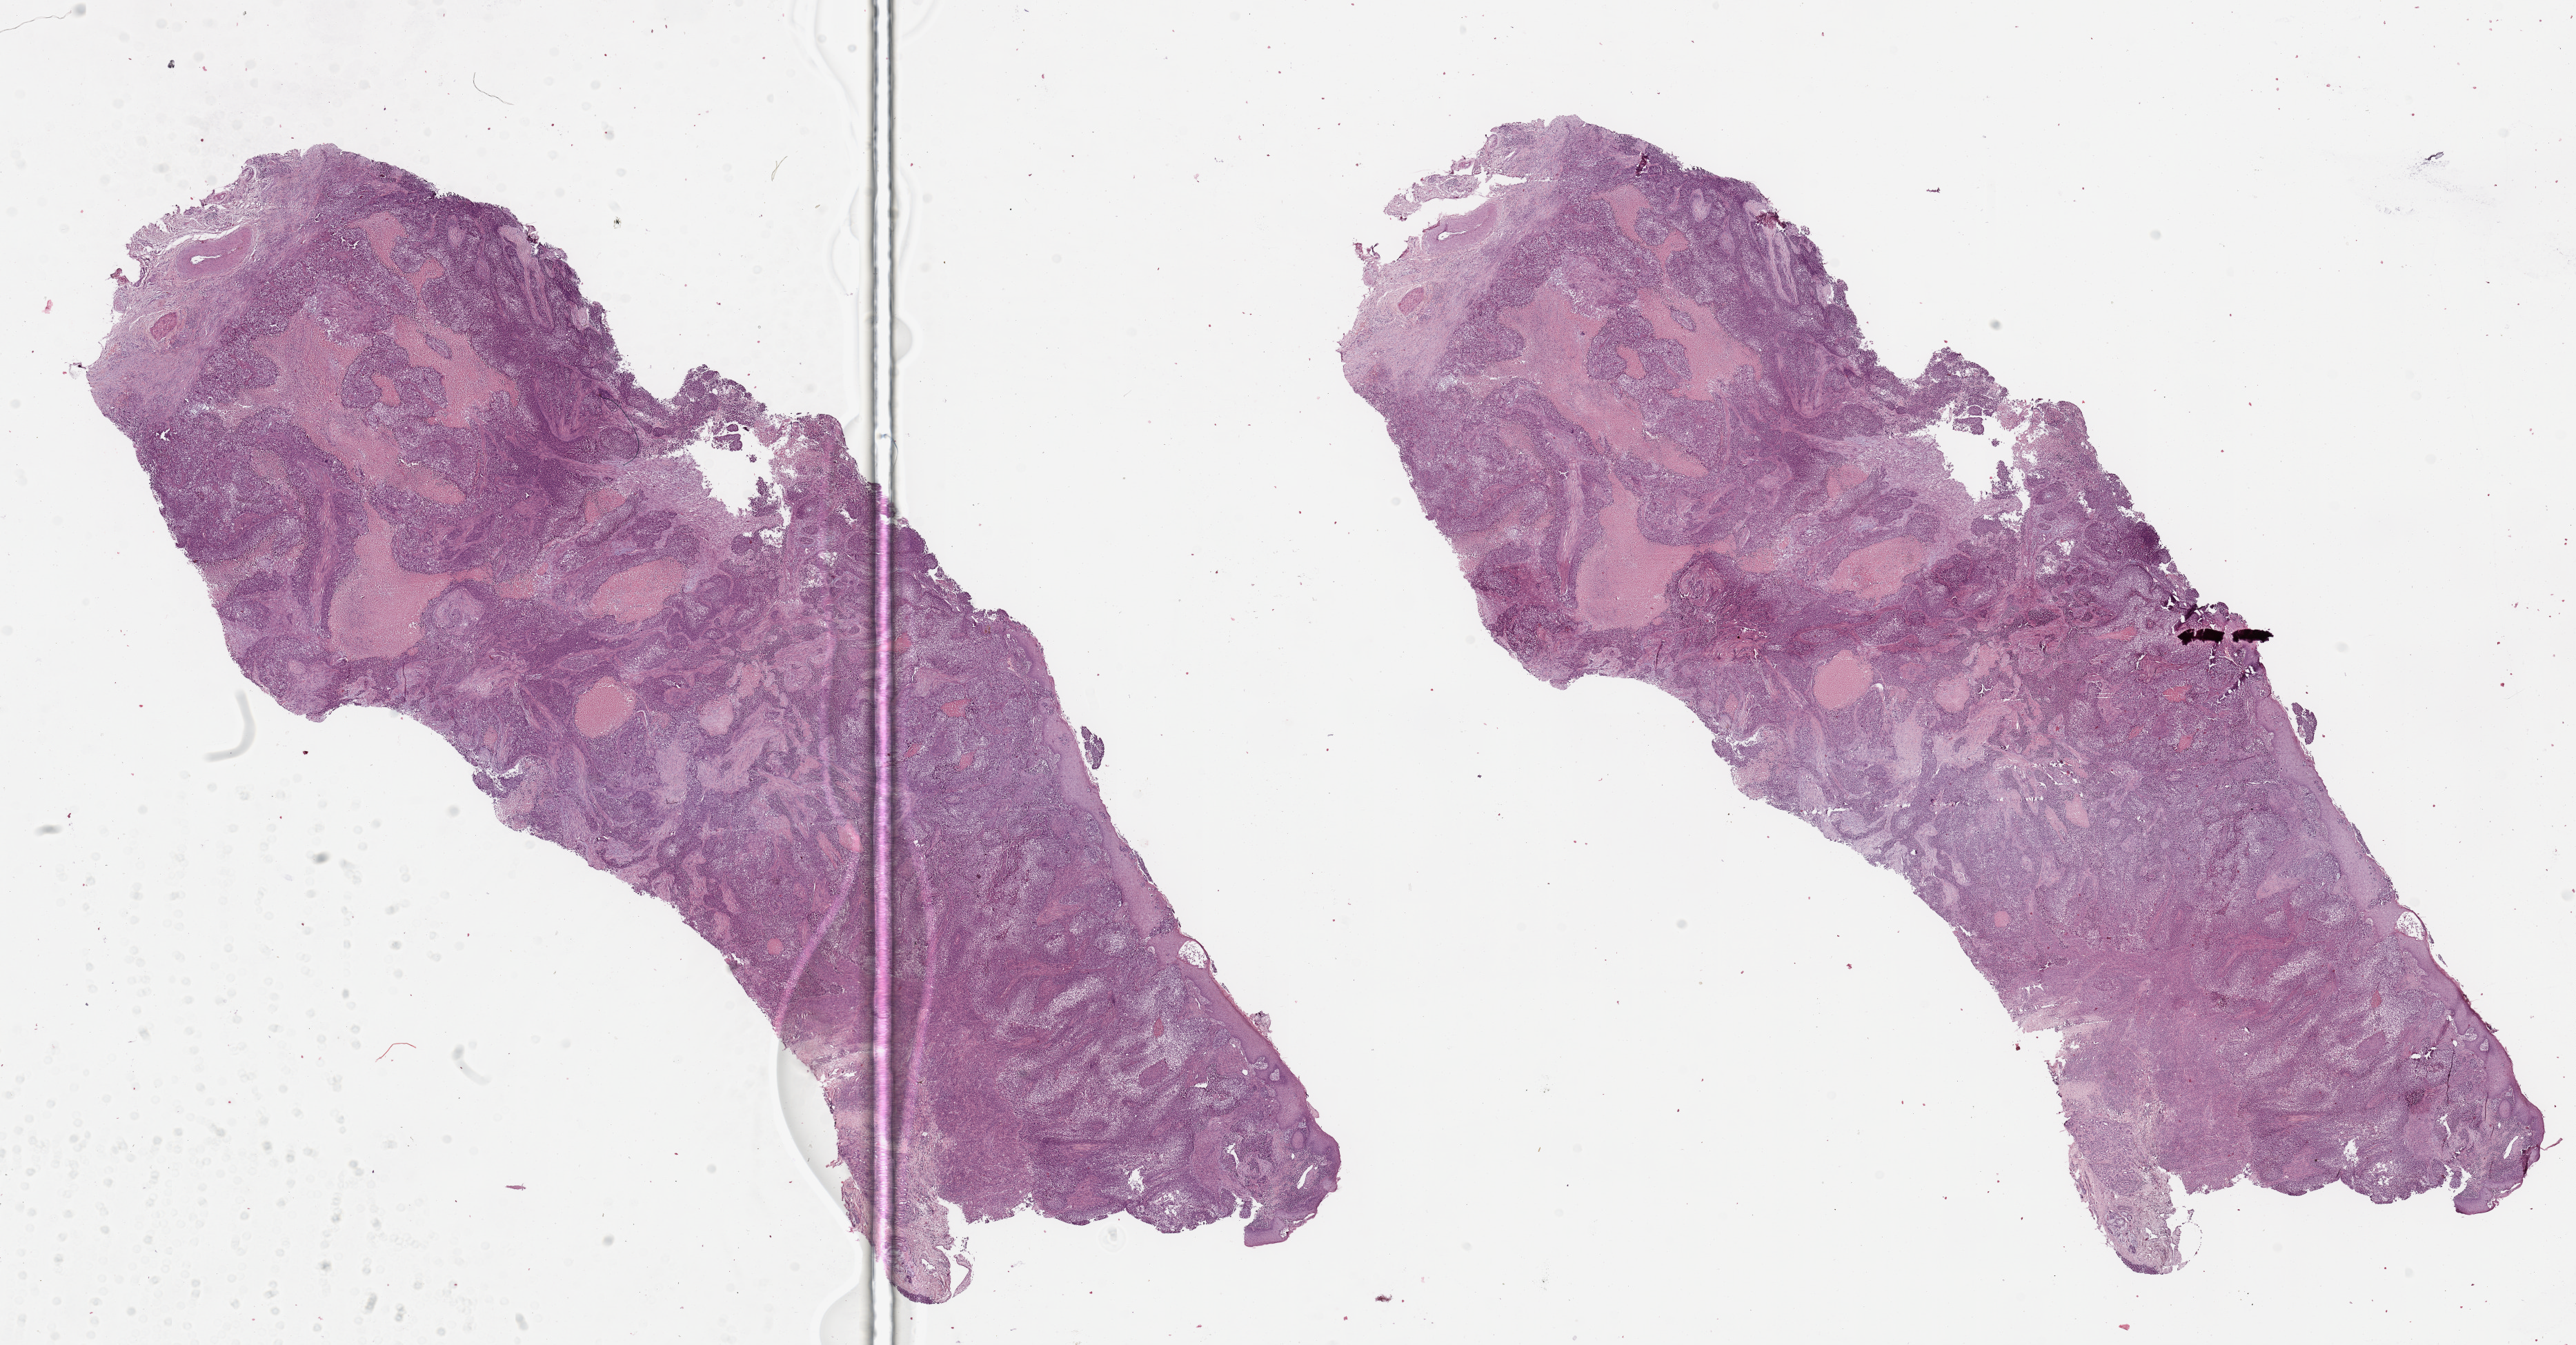
Whole-slide histology image, Hematoxylin and eosin (H&E) stained — shown as a low-resolution overview of the whole scanned area (about 29.5 x 15.4 mm). Head and neck, tissue type not recorded. 64-year-old male patient.
Patient diagnosis: Squamous cell carcinoma, NOS (larynx, NOS).